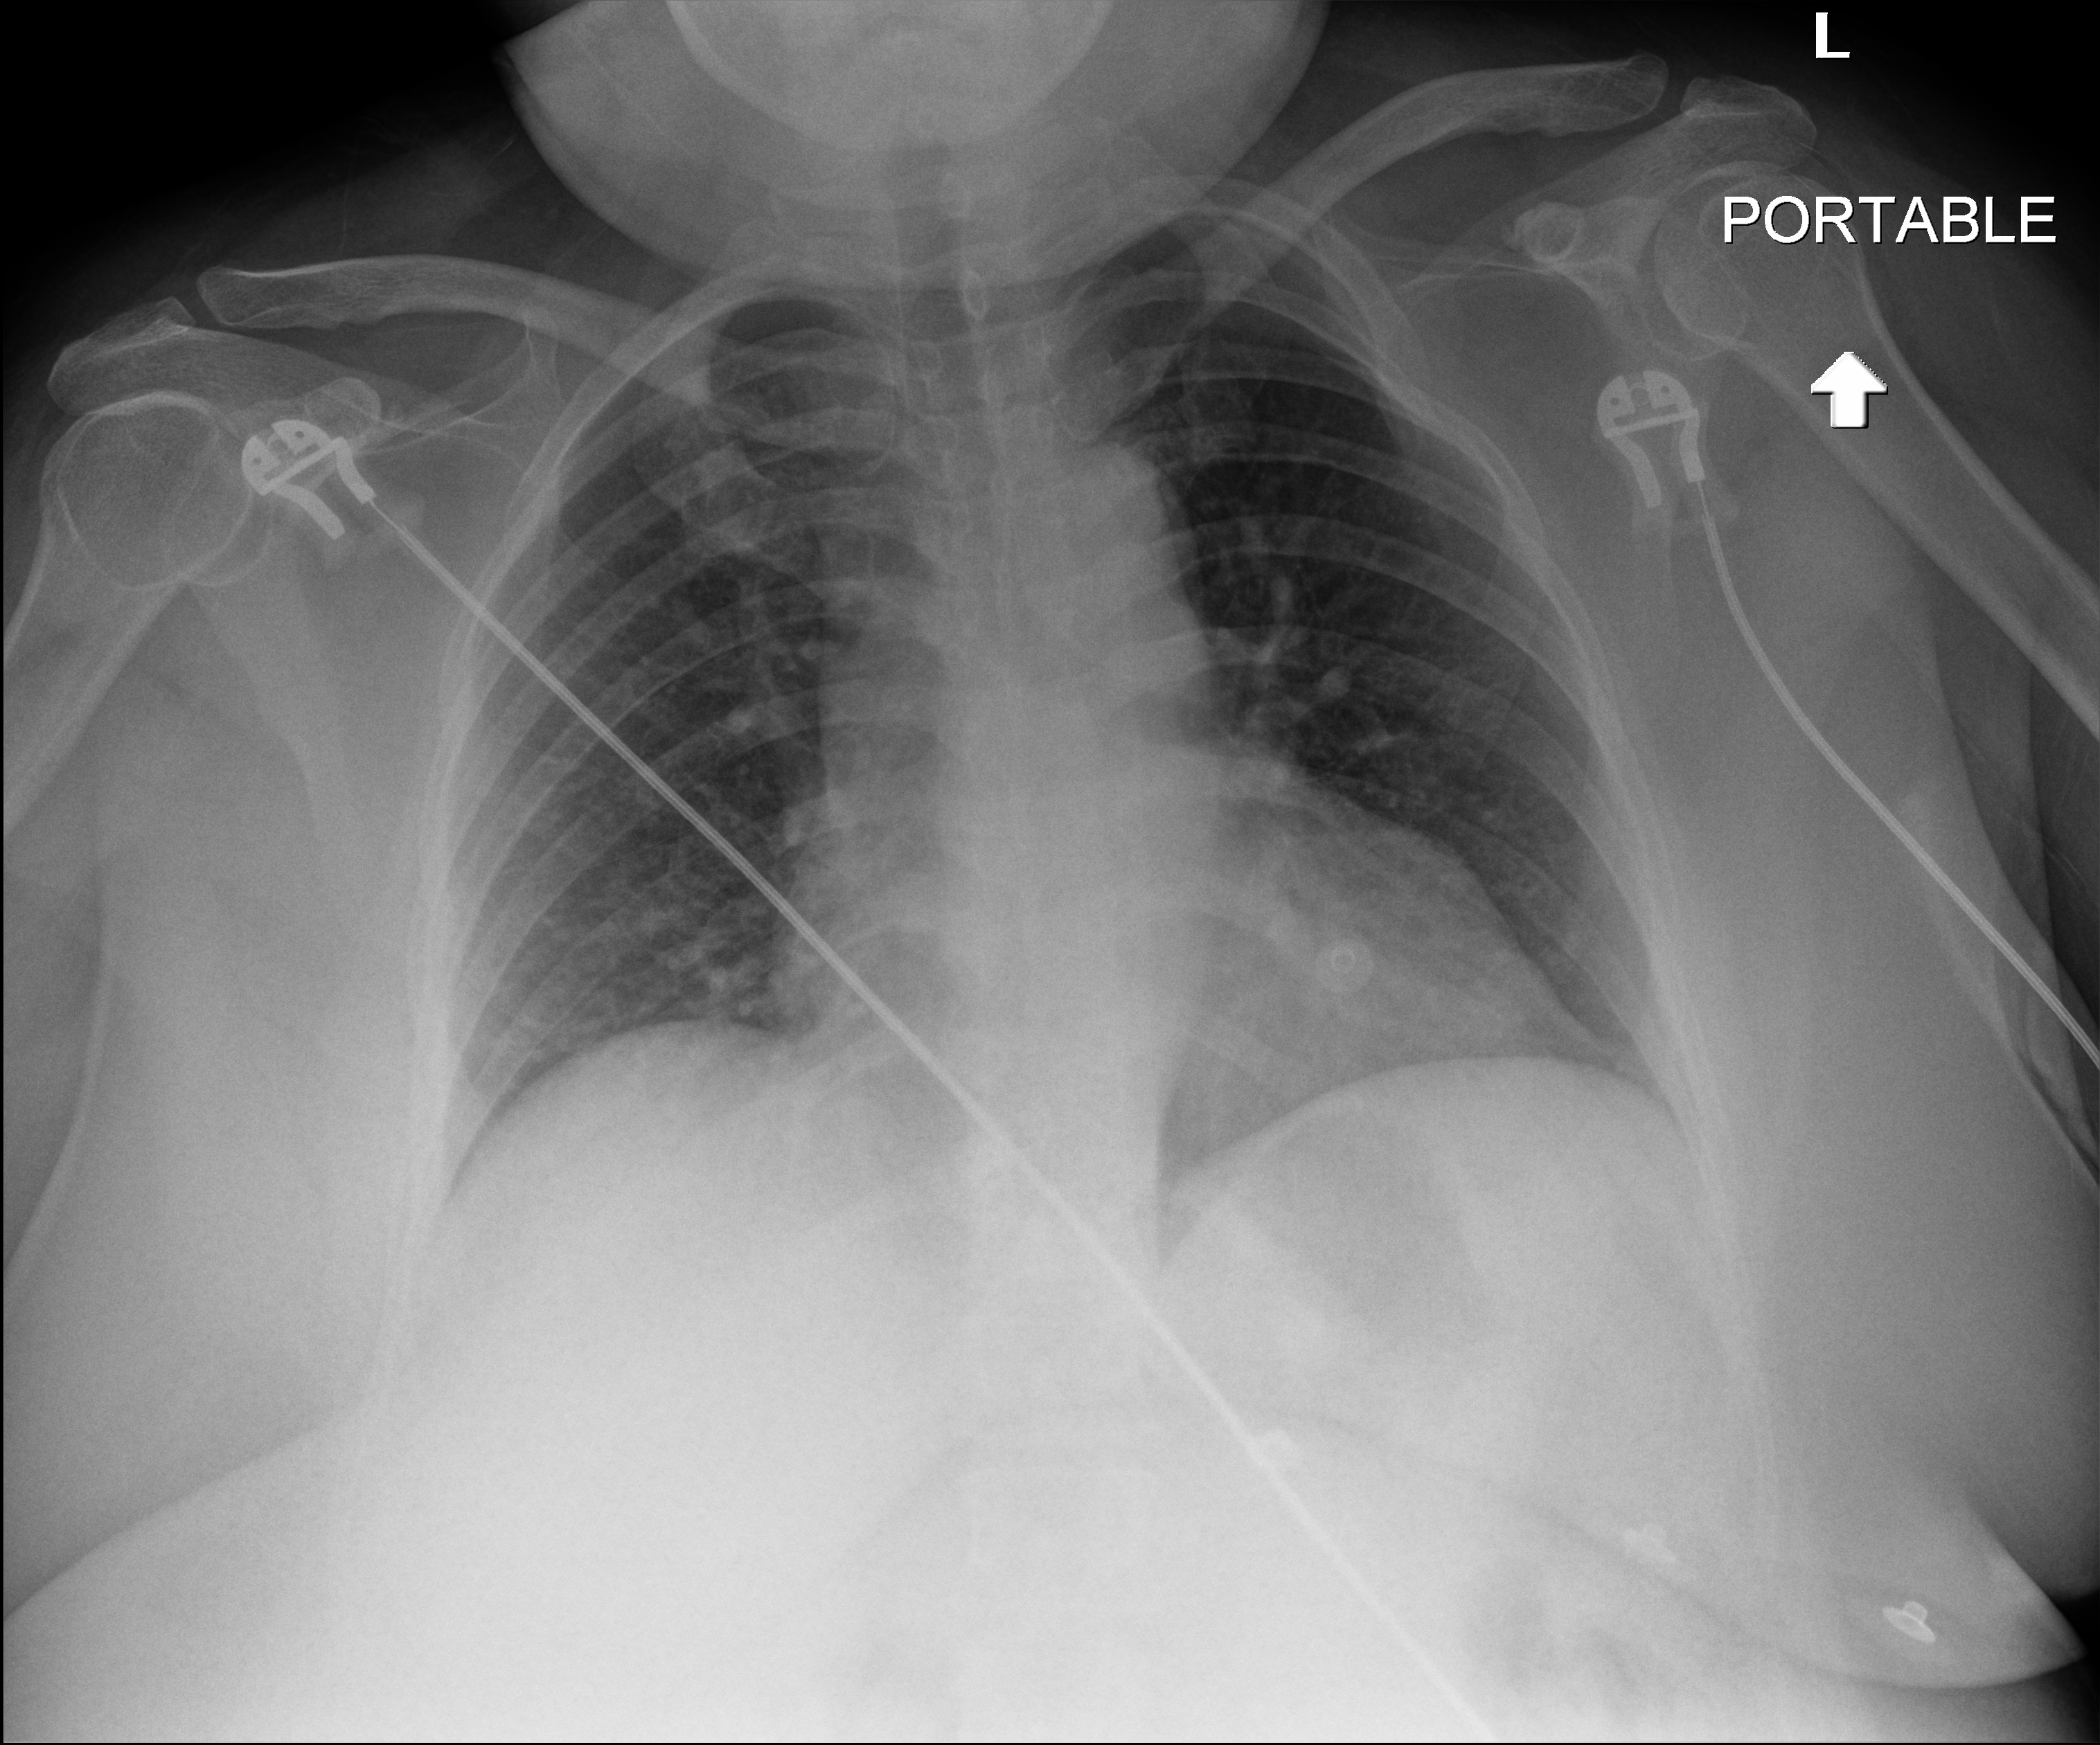
Chest radiograph; anteroposterior (AP) projection. Patient hospitalised with COVID-19; female, aged 18–59 years.
Admission-level facts for this patient (not findings on this image; timing relative to this image not recorded):
- length of hospital stay: 2 days